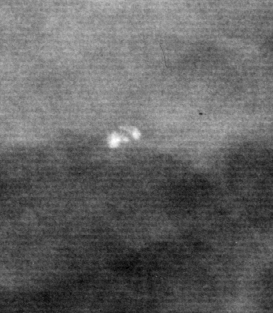
Cropped region of a digitized screen-film mammogram centred on a radiologist-marked abnormality, right breast, CC view.
Calcifications, morphology pleomorphic, distribution clustered; BI-RADS assessment category 3; pathology result (as recorded, not read from the image): benign.